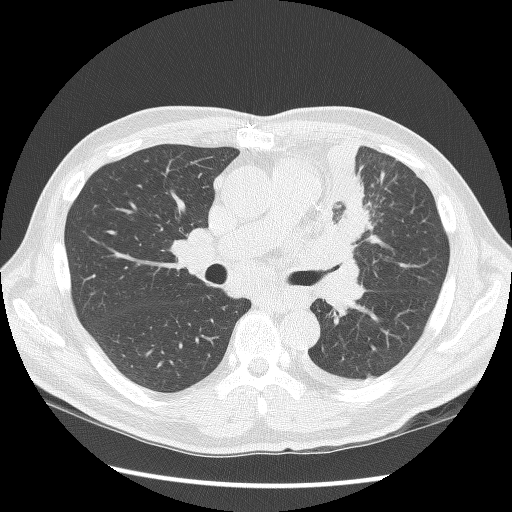
Chest CT (low-dose screening protocol), one axial image. Second annual screen. Lung window (W 1500 / L -600 HU). 2.5 mm slice thickness. 120 kVp. 512 × 512 image matrix, field of view 360 × 360 mm. Male participant, aged 64 years at enrolment. Former smoker at enrolment.
Expert-annotated lung lesion, bounding box <303,140,387,282> (left, top, right, bottom; pixels). Screening reader's record for this exam: no non-calcified nodule ≥4 mm recorded. Lung cancer was diagnosed 24 days after this screen: small cell carcinoma, NOS, left upper lobe, stage IV (AJCC 6th edition), 100 mm at pathology.